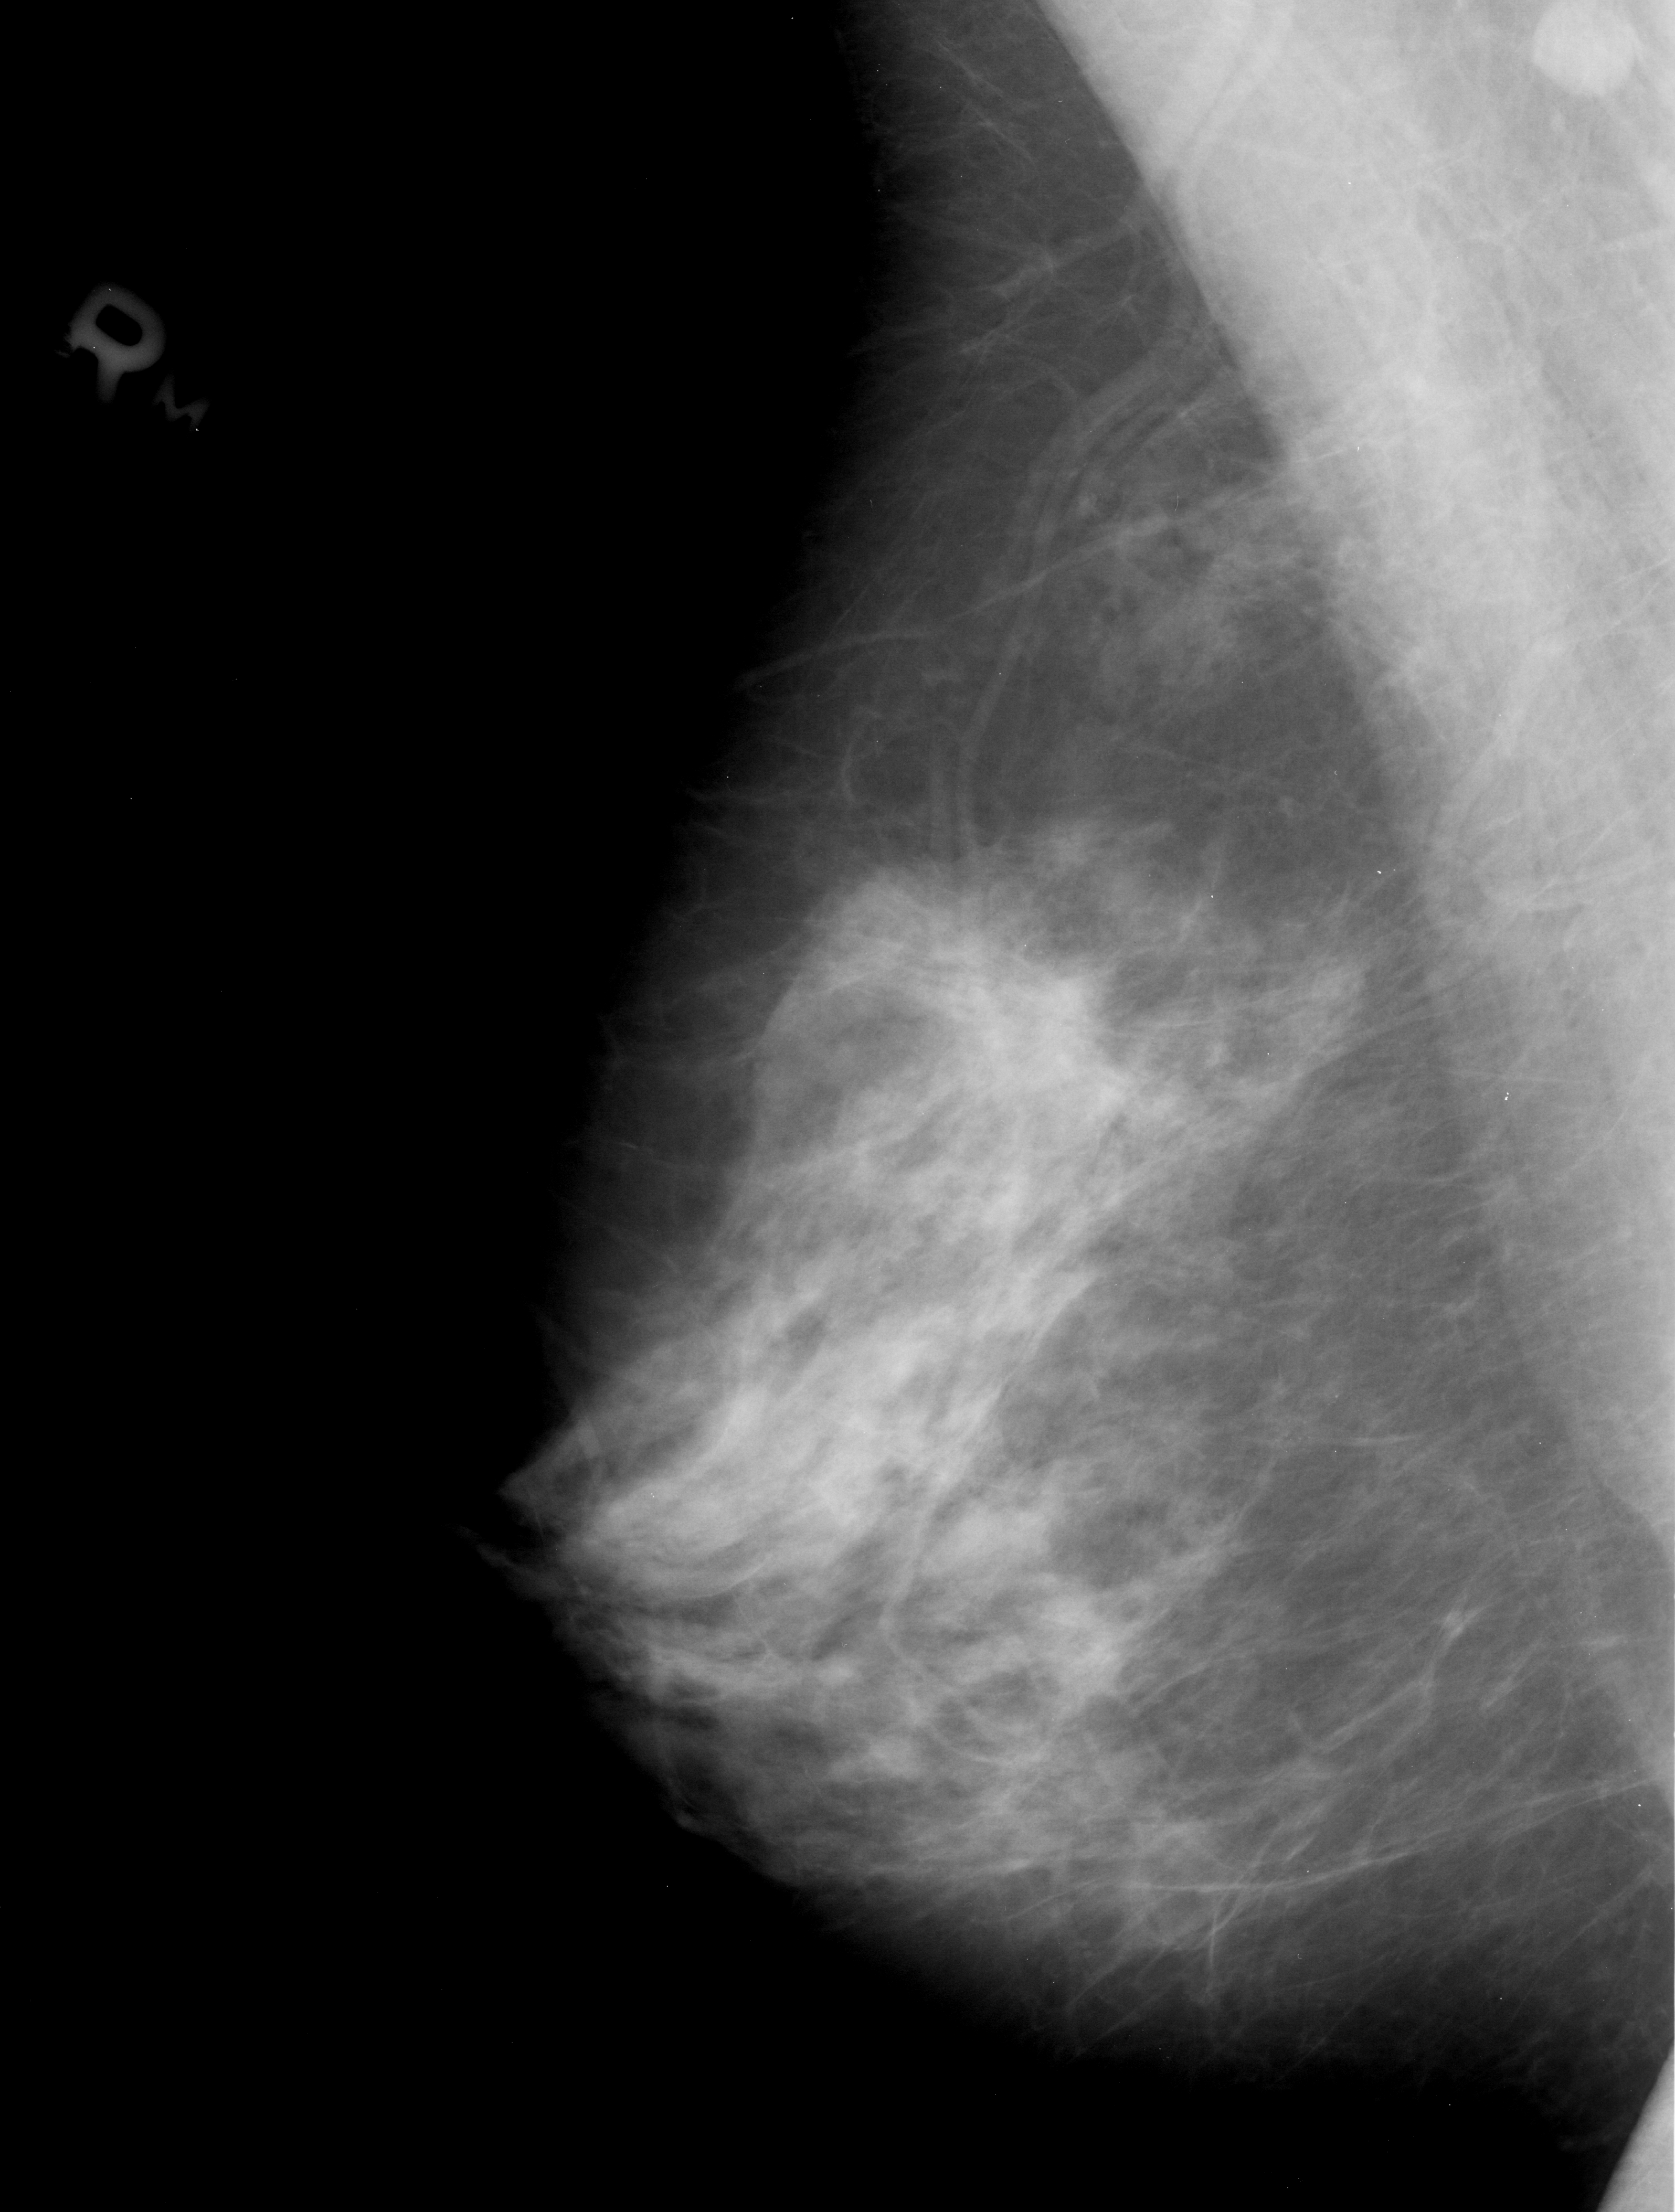
Scanned film-screen mammogram, right breast, mediolateral oblique (MLO) view, BI-RADS breast density category 3 (scale 1–4).
- Mass, shape irregular, margins spiculated; BI-RADS assessment category 4; subtlety rating 3 on a 1 (subtle) to 5 (obvious) scale; pathology (as recorded): malignant.